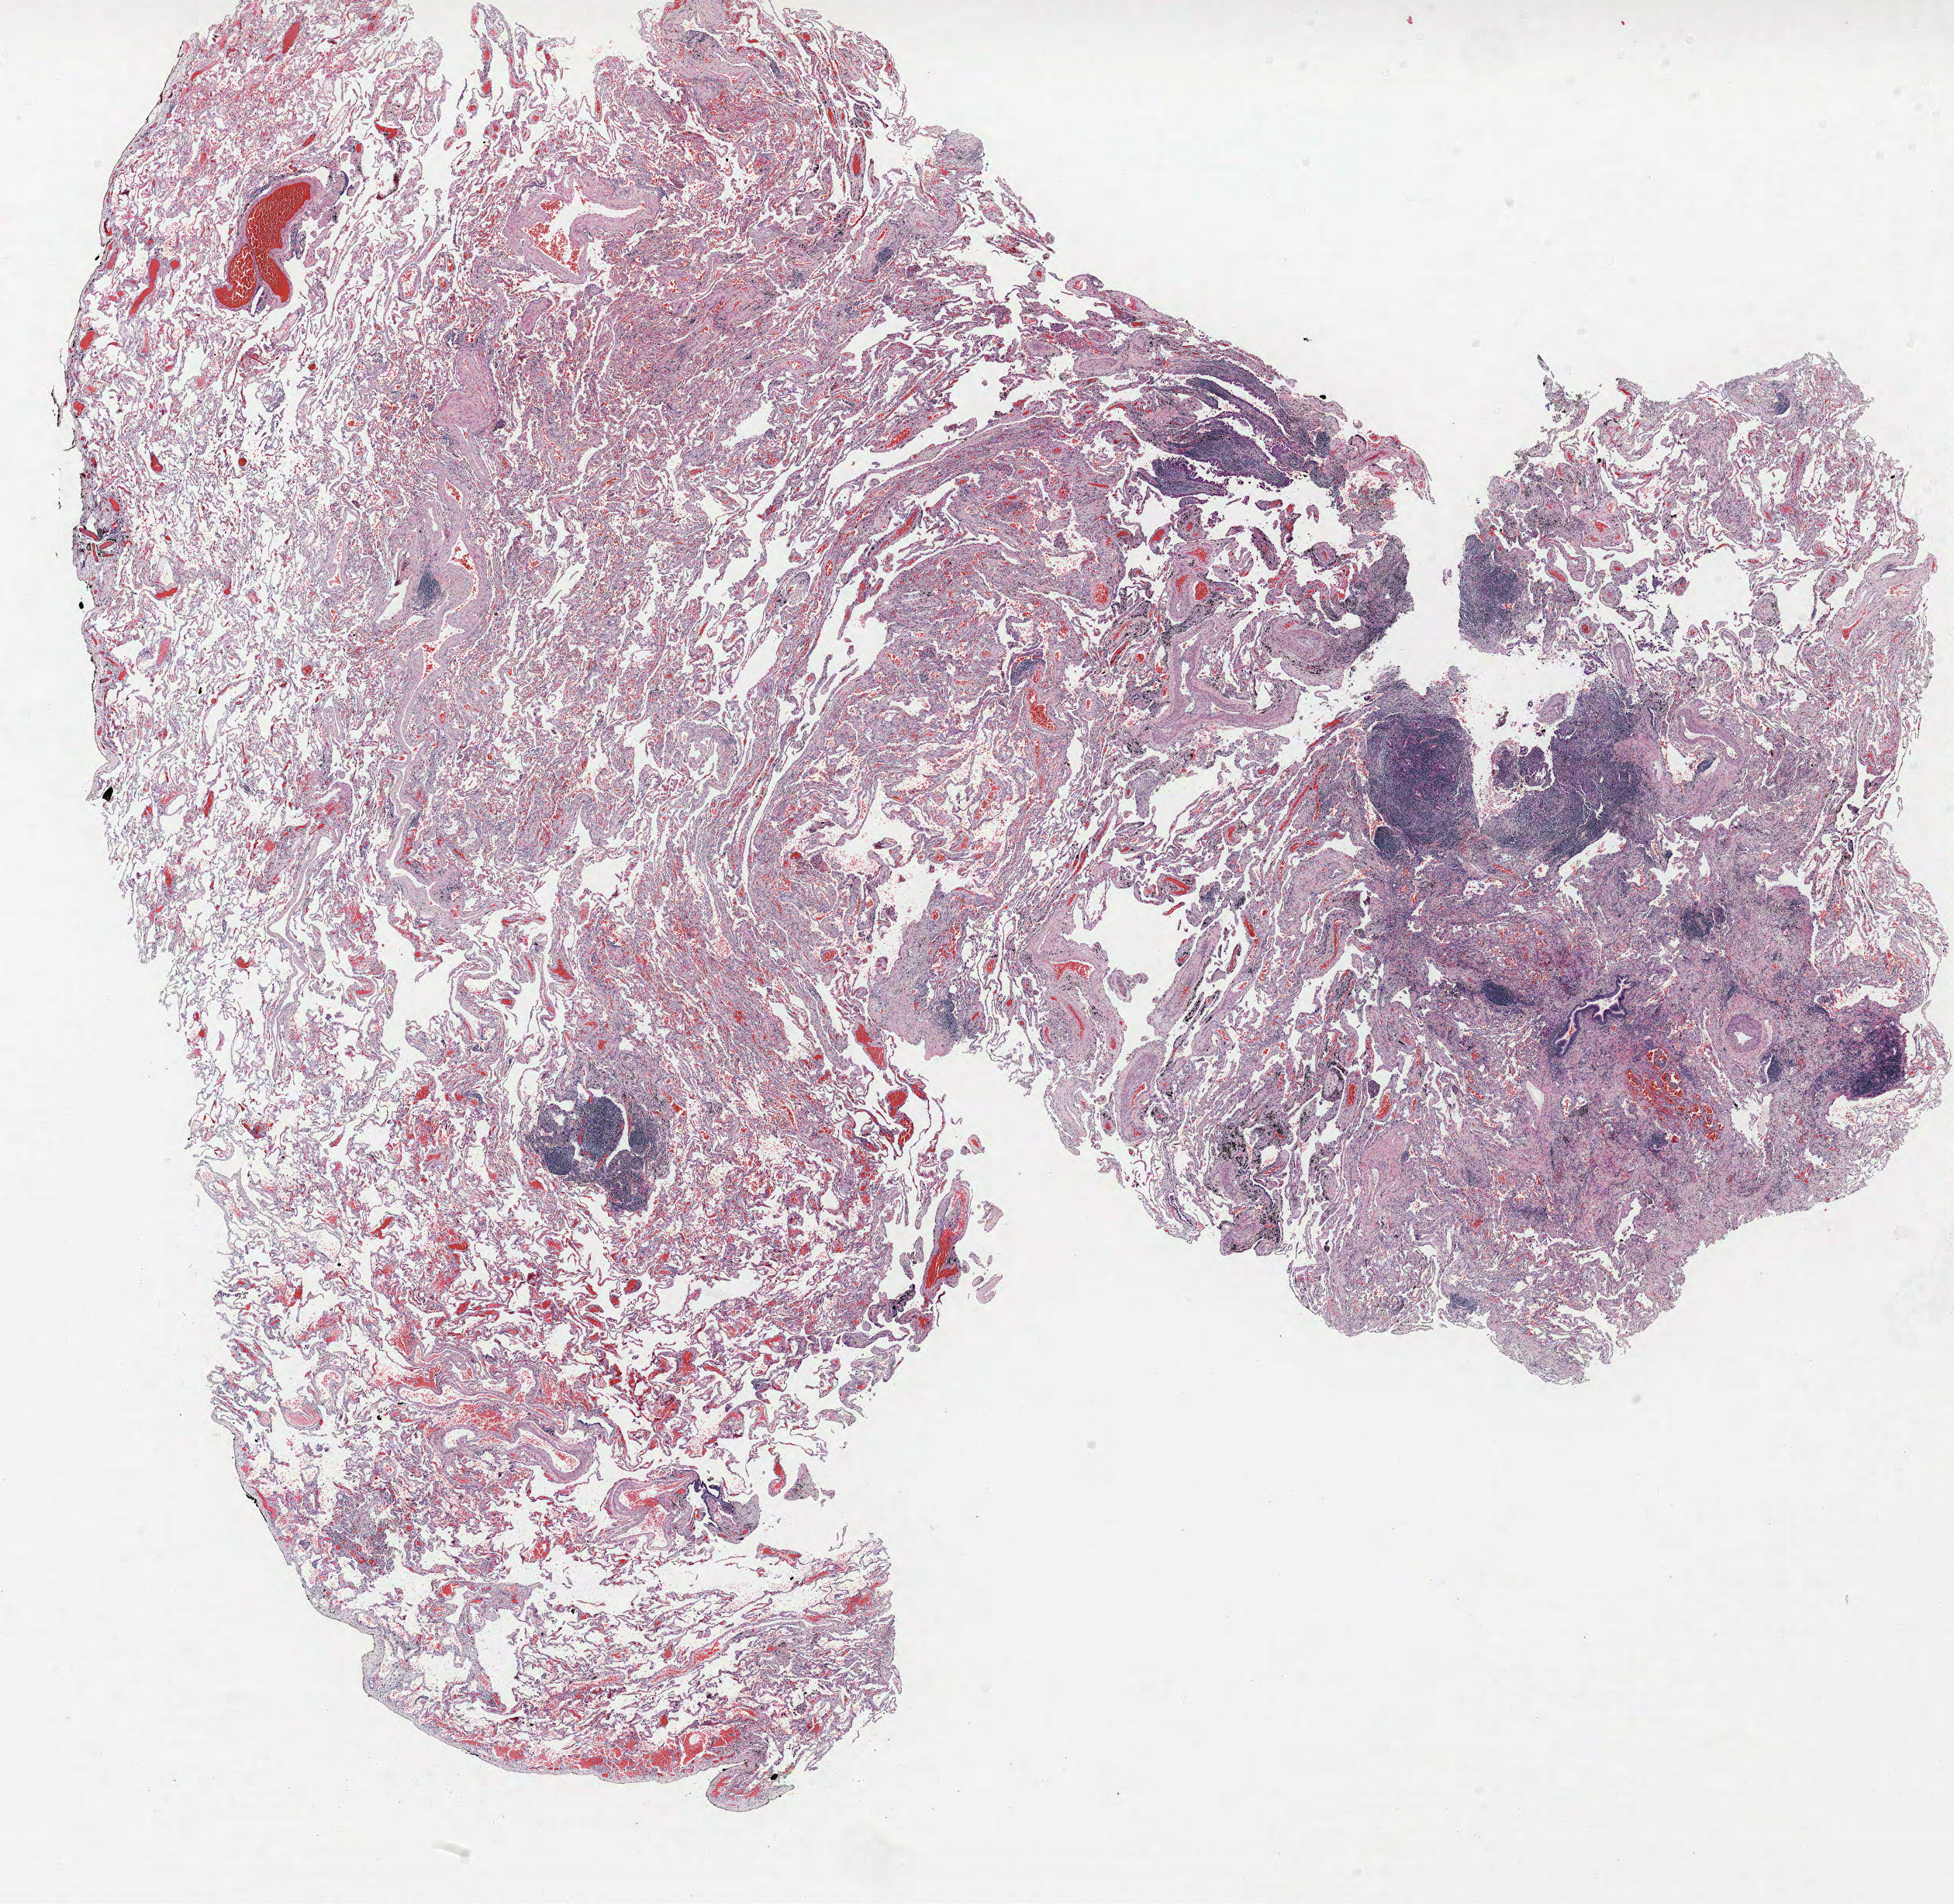
Whole-slide histology image, H&E — low-resolution overview of the scanned area, about 20.2 x 19.6 mm. FFPE section. Lung tissue. Female, age 67 at enrolment. Former smoker at enrolment. Grade: moderately differentiated (G2).
* primary tumour location (clinical record): right upper lobe
* stage (AJCC 6th edition): IA
* participant's lung-cancer diagnosis: Adenocarcinoma, NOS (ICD-O-3 8140/3)
* tumour size (pathology): 14 mm